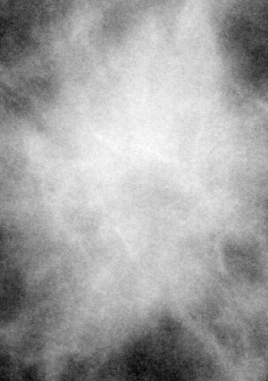
Cropped region of a digitized screen-film mammogram centred on a radiologist-marked abnormality; right breast; CC view.
Mass, shape irregular, margins spiculated; BI-RADS assessment category 5; subtlety rating 5 on a 1 (subtle) to 5 (obvious) scale; pathology (as recorded): malignant.